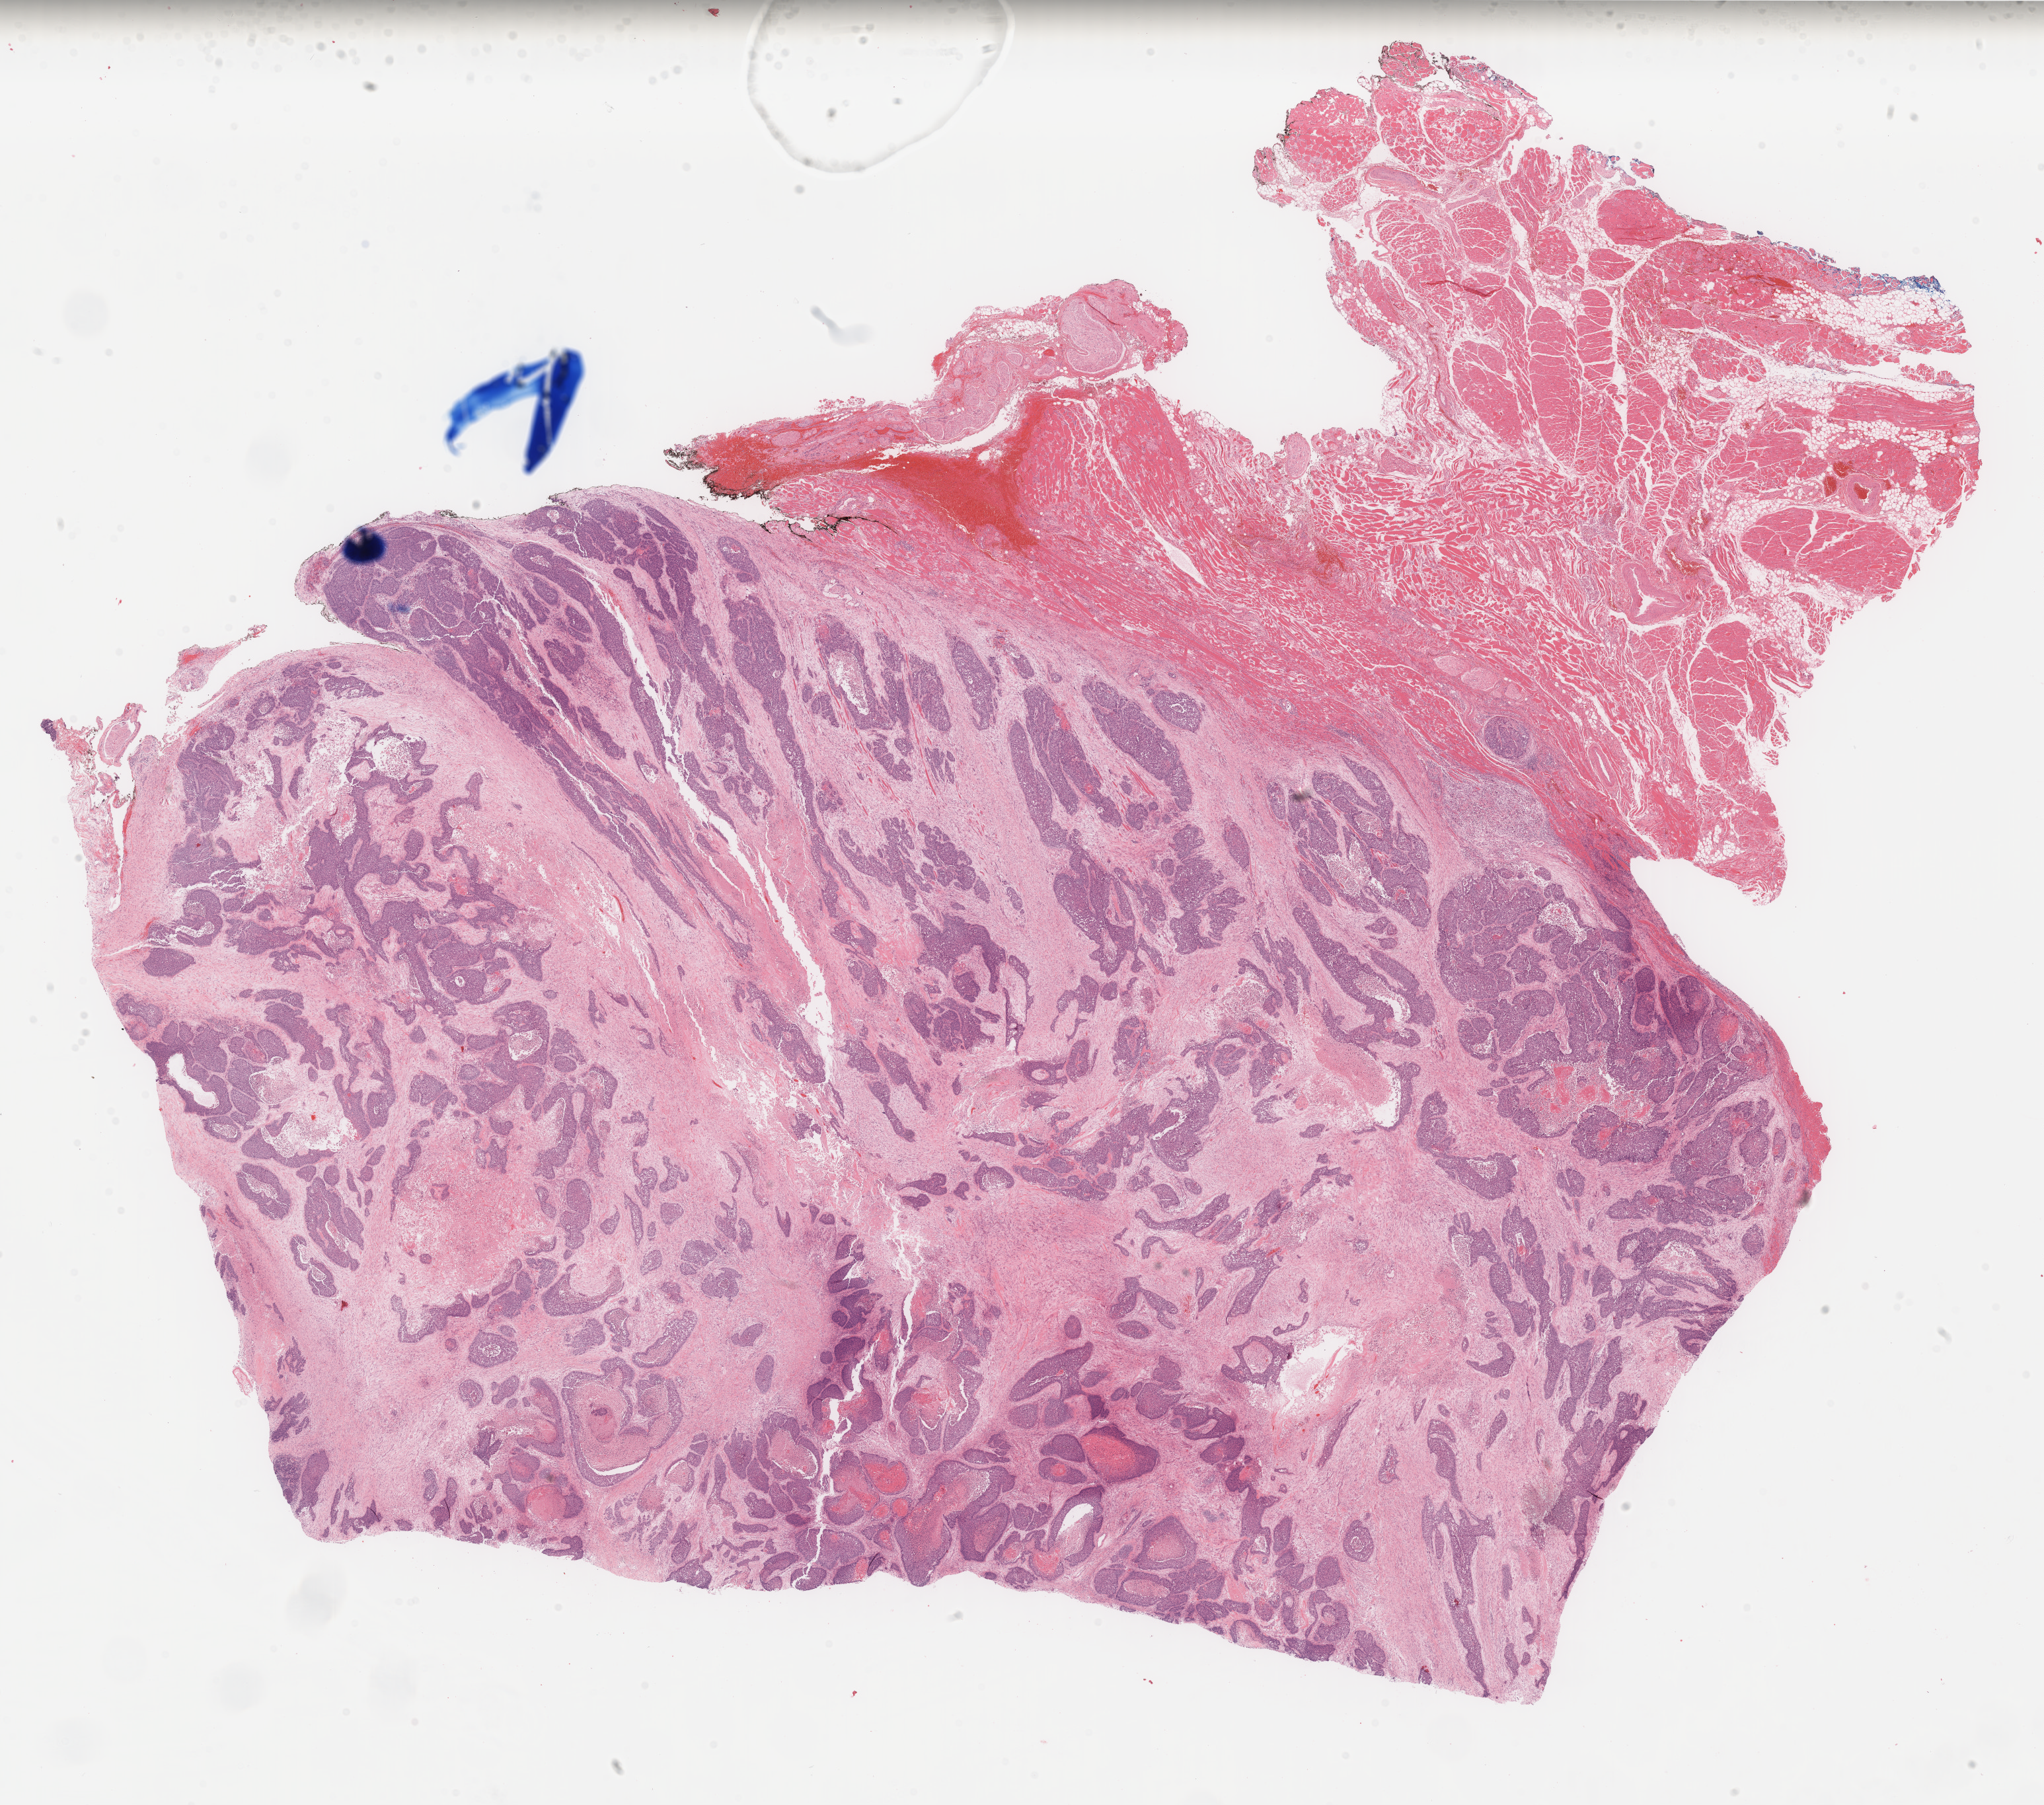
Digitized Hematoxylin and eosin (H&E) stained tissue section (whole slide), shown as a low-resolution overview of the whole scanned area (about 24.5 x 21.6 mm). Formalin-fixed paraffin-embedded (FFPE) diagnostic section. Sample: primary tumour, head and neck. Male patient; age at initial diagnosis 59 years. Histologic grade: G2 (moderately differentiated).
• diagnosis: Squamous cell carcinoma, NOS (floor of mouth, NOS)
• laterality: right
• AJCC pathologic stage: IVA (7th edition)